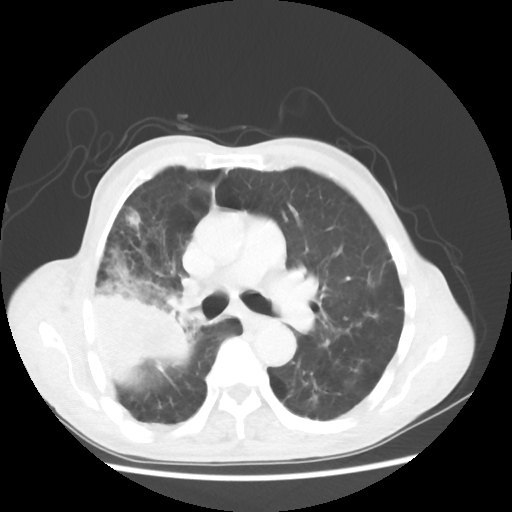
Chest CT, one axial slice. Slice 32 of 58 in the series (ordered by position). Reconstruction kernel STANDARD. 100 kVp. Lung window (W 1500 / L -600 HU). 512 × 512 image matrix. Male patient, age 75 years. From the clinical record (not read from this slice): clinical TNM (as recorded): T4 N1 M1.
Annotated regions visible in this slice (bounding box drawn by a radiologist):
- lung tumour (recorded histology: adenocarcinoma): bounding box (x1, y1, x2, y2) in pixels: (84, 274, 204, 386)